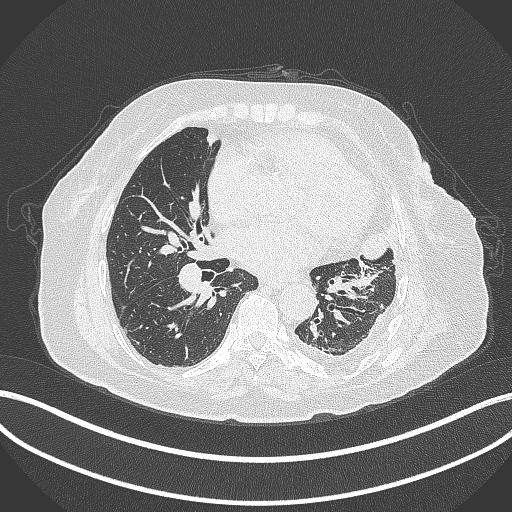
Chest CT, one axial slice. Position 167 of 399 along the scan axis. Reconstruction kernel B70f. Lung window (W 1500 / L -600 HU). 1 mm slice thickness. 512 × 512 image matrix. Female patient, age 75 years. From the clinical record (not read from this slice): clinical TNM (as recorded): T3 N3 M1.
Structures marked on this image (bounding box drawn by a radiologist):
- lung tumour (recorded histology: adenocarcinoma): bounding box (x1, y1, x2, y2) in pixels: (356, 219, 402, 261)